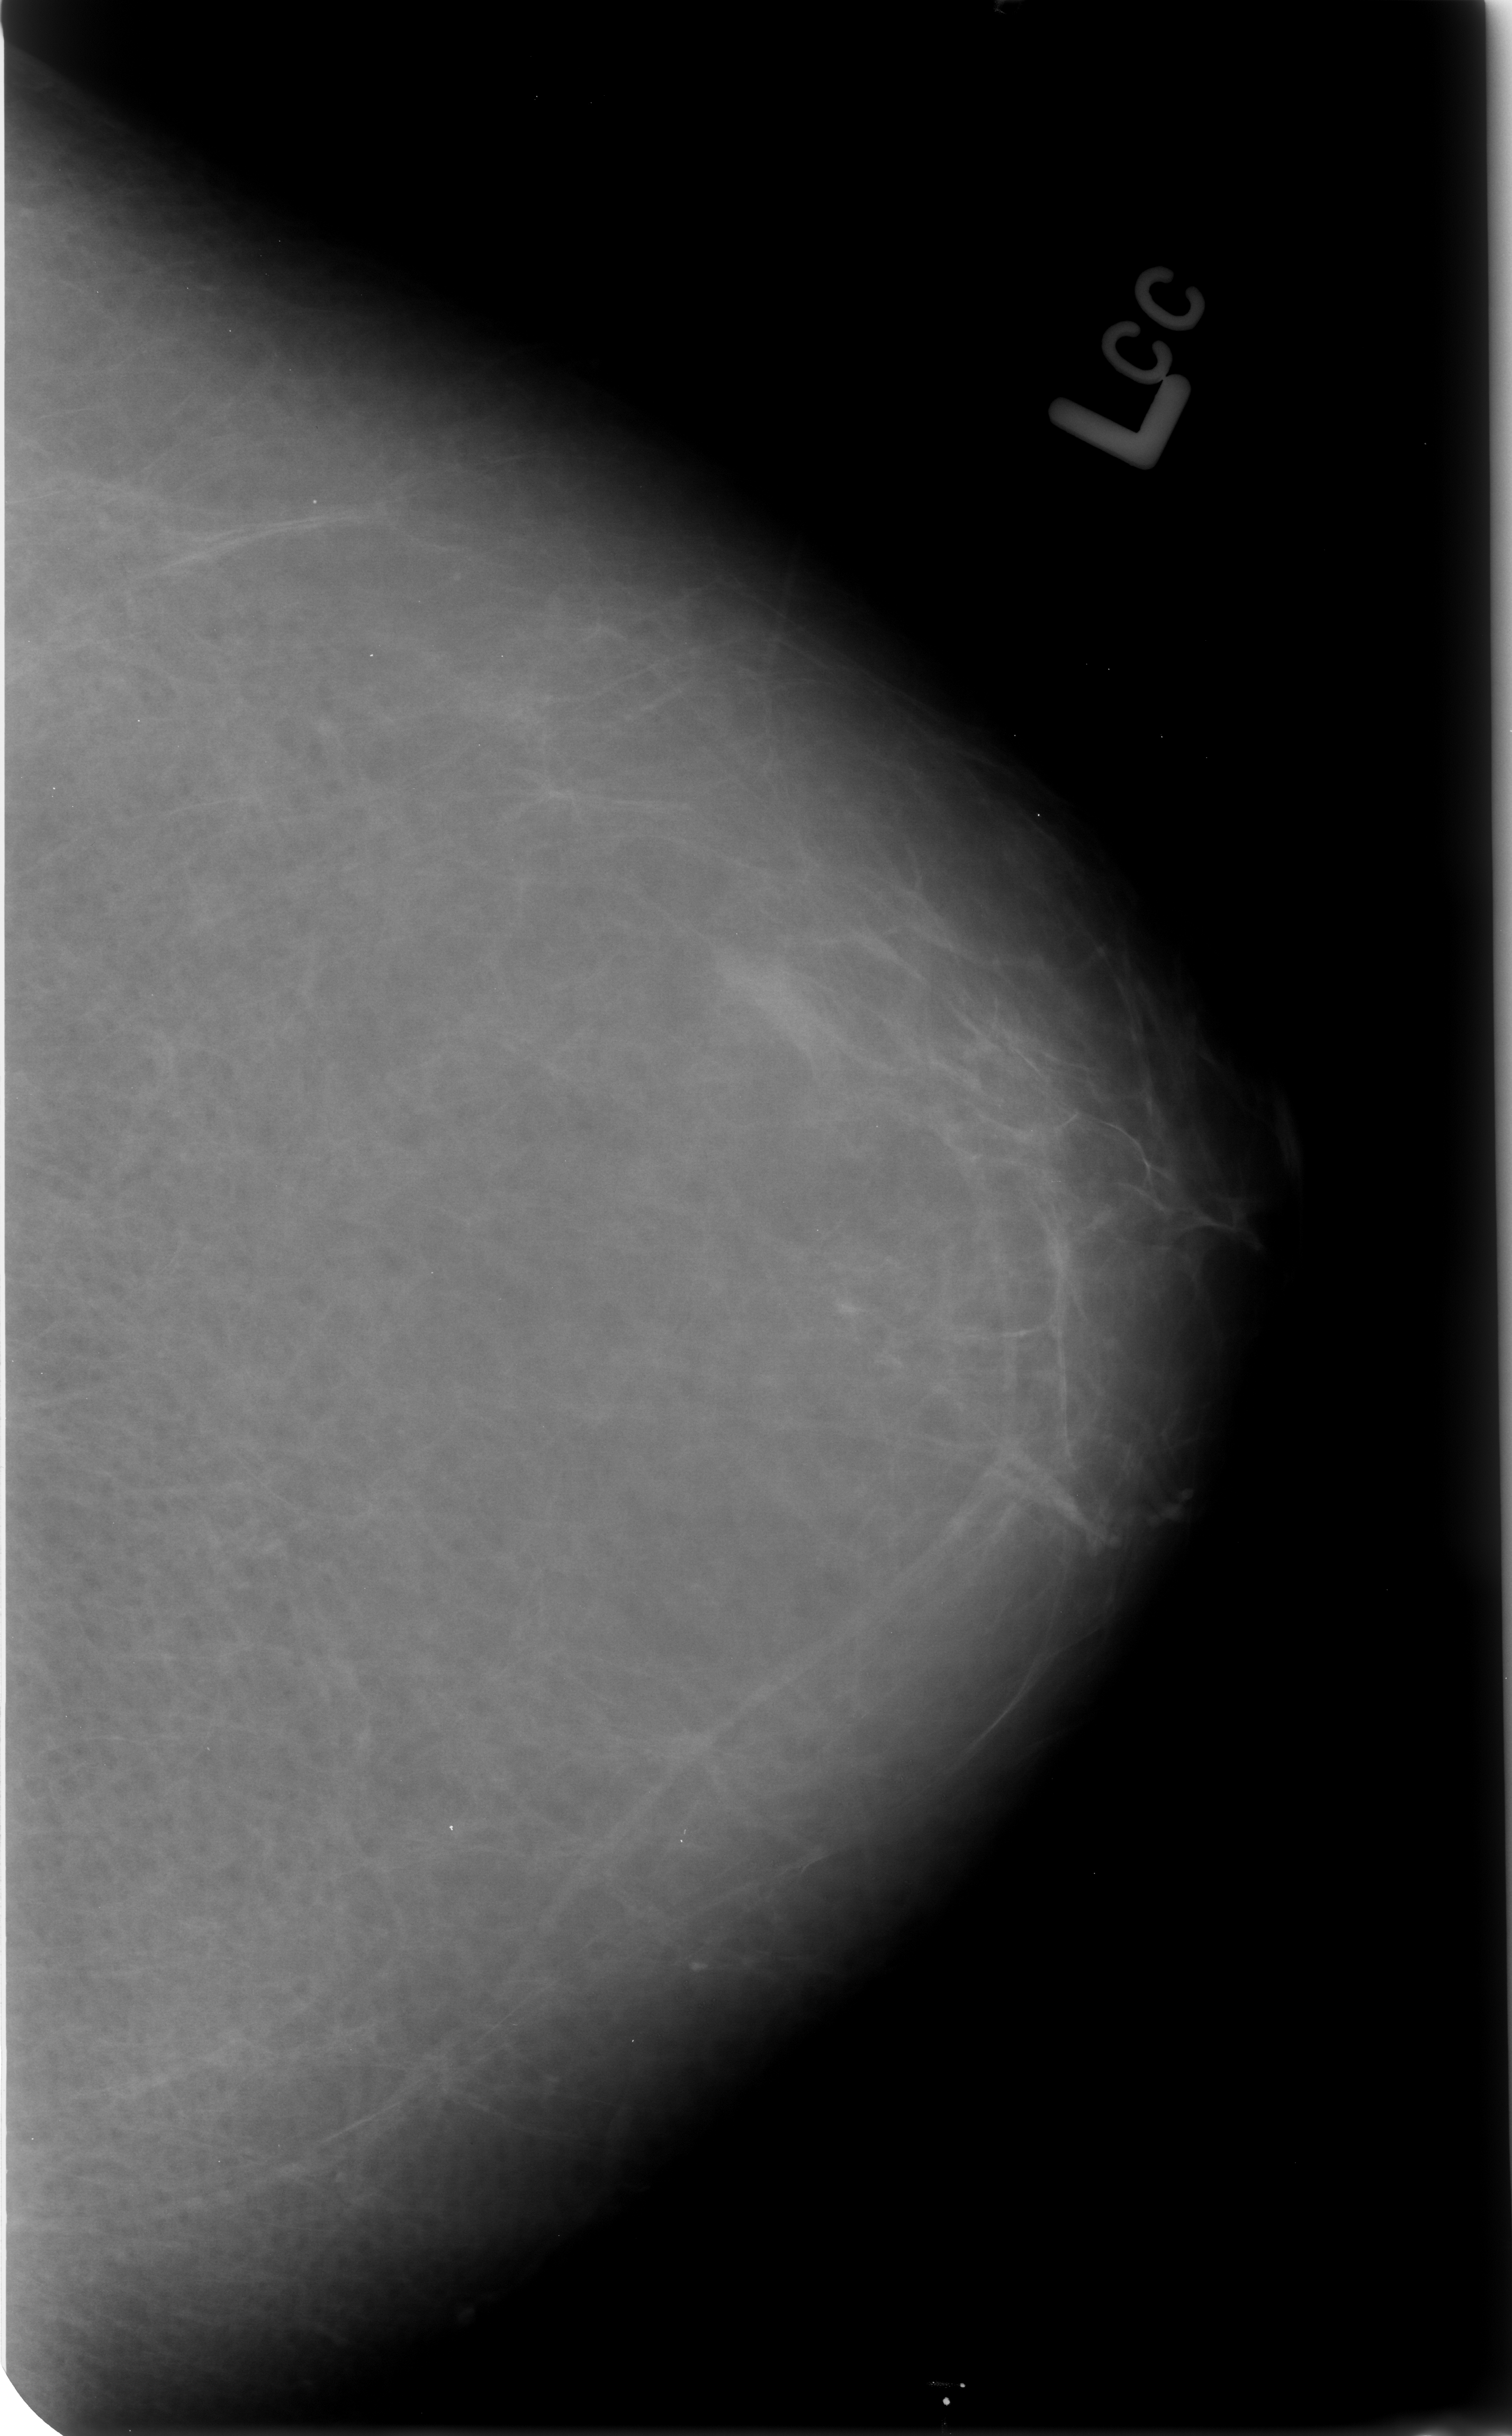
Digitized screen-film mammogram; left breast; CC view; BI-RADS breast density category 1 (scale 1–4).
Mass, shape irregular, margins ill defined; BI-RADS assessment category 4; subtlety rating 4 on a 1 (subtle) to 5 (obvious) scale; pathology (as recorded): benign.